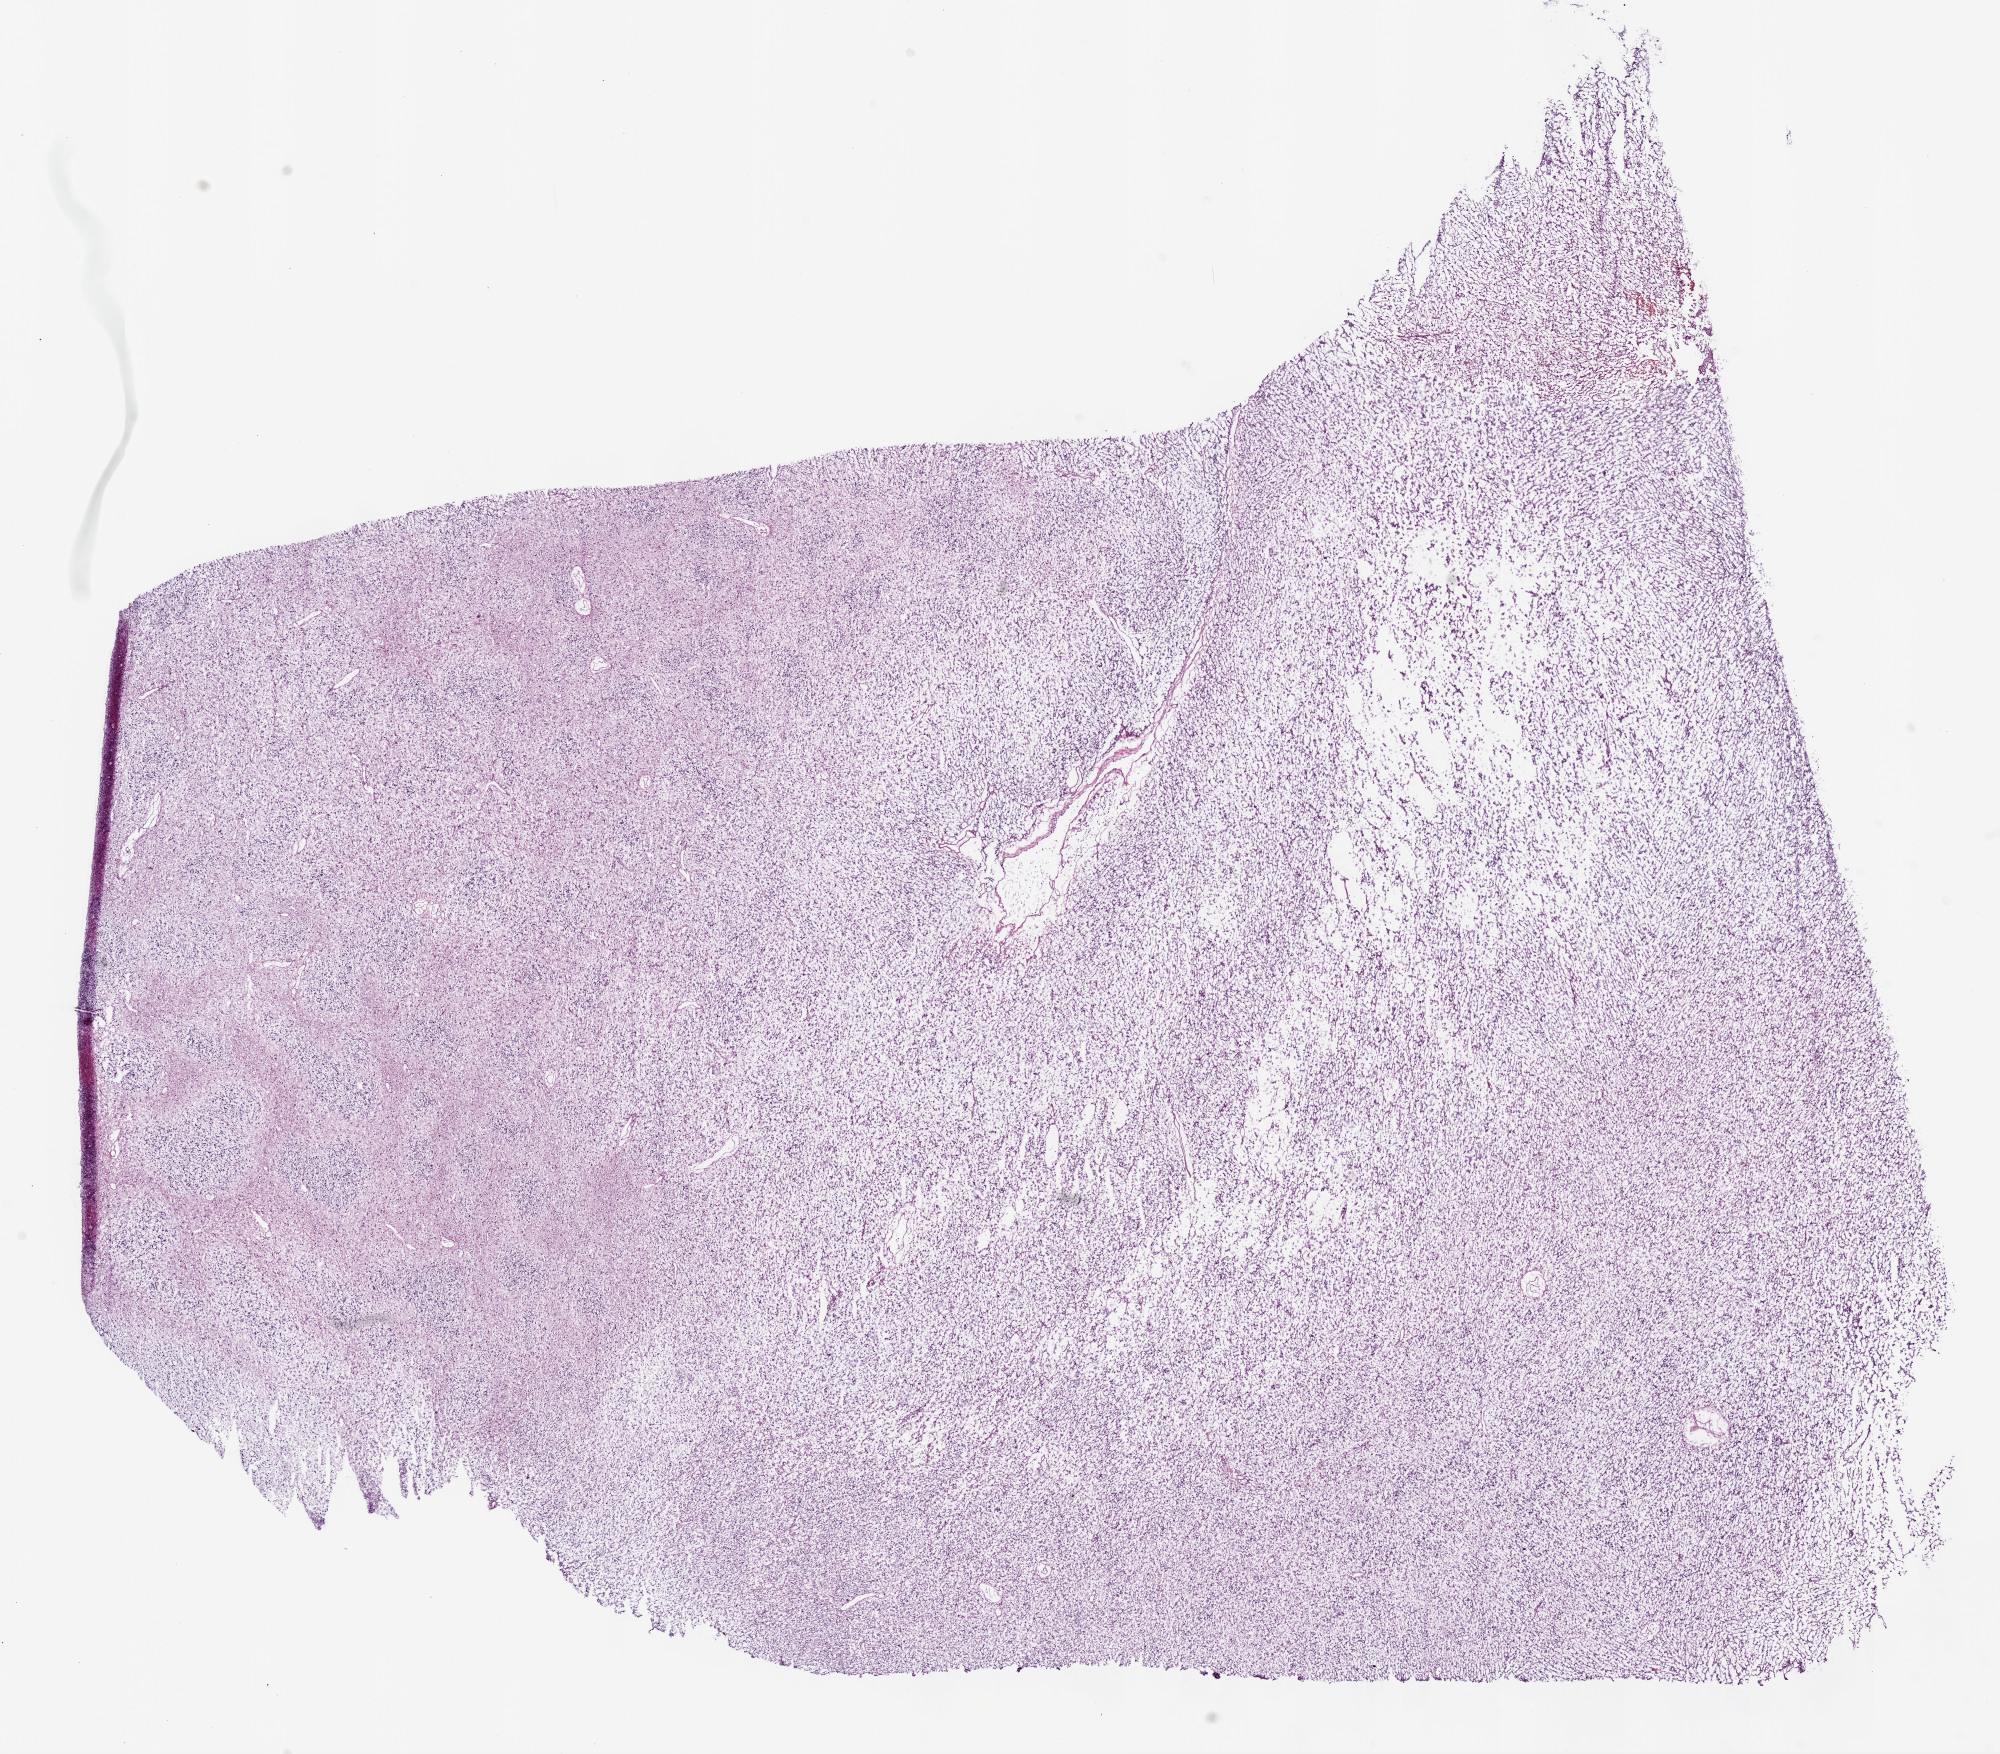
Digitized Hematoxylin and eosin (H&E) stained tissue section (whole slide) — low-resolution overview of the scanned area, about 16.0 x 14.1 mm (acquisition: 20x scan), frozen section from the top of the tissue portion, primary tumour sample from the brain. Male, age 36 years at initial diagnosis. Pathologist review of this section (percent, as recorded): tumour cells 100%, tumour nuclei 65%.
Pathologic diagnosis: Mixed glioma.